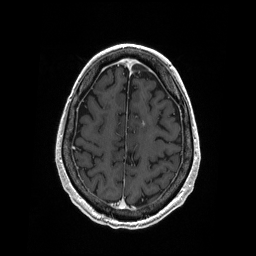
Brain MRI from a brain-tumour surgery series, one axial slice; slice 62 of 208 in the series (ordered by position); T1-weighted post-contrast; 1 mm slice thickness; 256 × 256 image matrix. Case-level facts recorded for this patient, not image findings: histopathology: Primary diffuse large B-cell lymphoma; tumour location: Left Corpus Callosum (Frontal).
Annotated regions visible in this slice (expert manual segmentation):
- tumour: bounding box <142,120,146,127> (left, top, right, bottom; pixels)